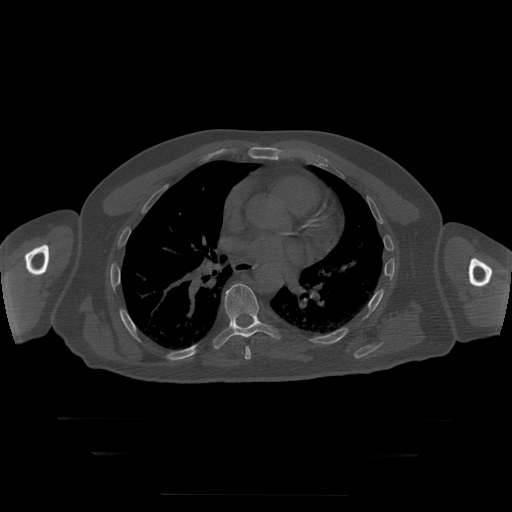
CT including the spine, one axial slice. Position 169 of 397 along the scan axis. Reconstruction kernel STANDARD. Bone window (W 1800 / L 400 HU). 1.25 mm slice thickness. 512 × 512 image matrix, field of view 510 × 510 mm. Patient age 73 years. Case-level facts recorded for this patient, not image findings: primary cancer: prostate.
Structures marked on this image (semi-automatically segmented with operator editing):
- T7 vertebra: box from (x=245, y=347) to (x=251, y=360) px
- T8 vertebra: (x=213, y=284)–(x=281, y=350)